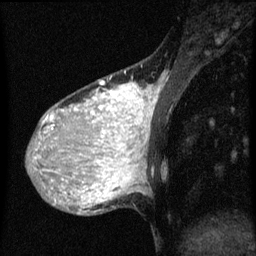
Breast MRI (dynamic contrast-enhanced), one sagittal slice; position 15 of 60 along the scan axis; dynamic contrast-enhanced series, image 2 of 3 at this slice position (ordered by acquisition); 1.5 T; TE 4.2 ms, TR 8 ms; 2 mm slice thickness; 256 × 256 image matrix, field of view 180 × 180 mm. Patient: female, 36 years.
Annotated regions visible in this slice (semi-automatically segmented with operator editing):
- analysis volume of interest (the breast-tissue region the enhancement analysis was run in; not a lesion): bounding box [x1, y1, x2, y2] px = [32, 70, 161, 161]
- tumour enhancement mask (voxels above the 70 % enhancement threshold inside the analysis volume of interest): [36, 82, 155, 161]